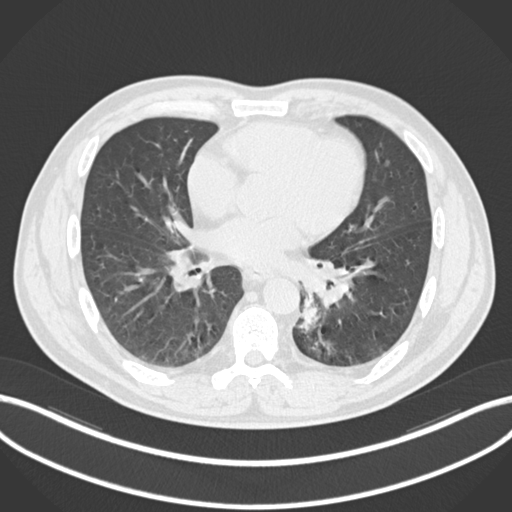
Chest CT, one axial slice. Position 99 of 223 along the scan axis. 120 kVp. Lung window (W 1500 / L -600 HU). 512 × 512 image matrix, field of view 400 × 400 mm. Patient: male, 50 years. From the clinical record (not read from this slice): clinical TNM (as recorded): T2a N3 M0.
Annotated regions visible in this slice (rectangle marked by the reading radiologist):
- lung tumour (recorded histology: squamous cell carcinoma): box from (x=297, y=294) to (x=325, y=336) px